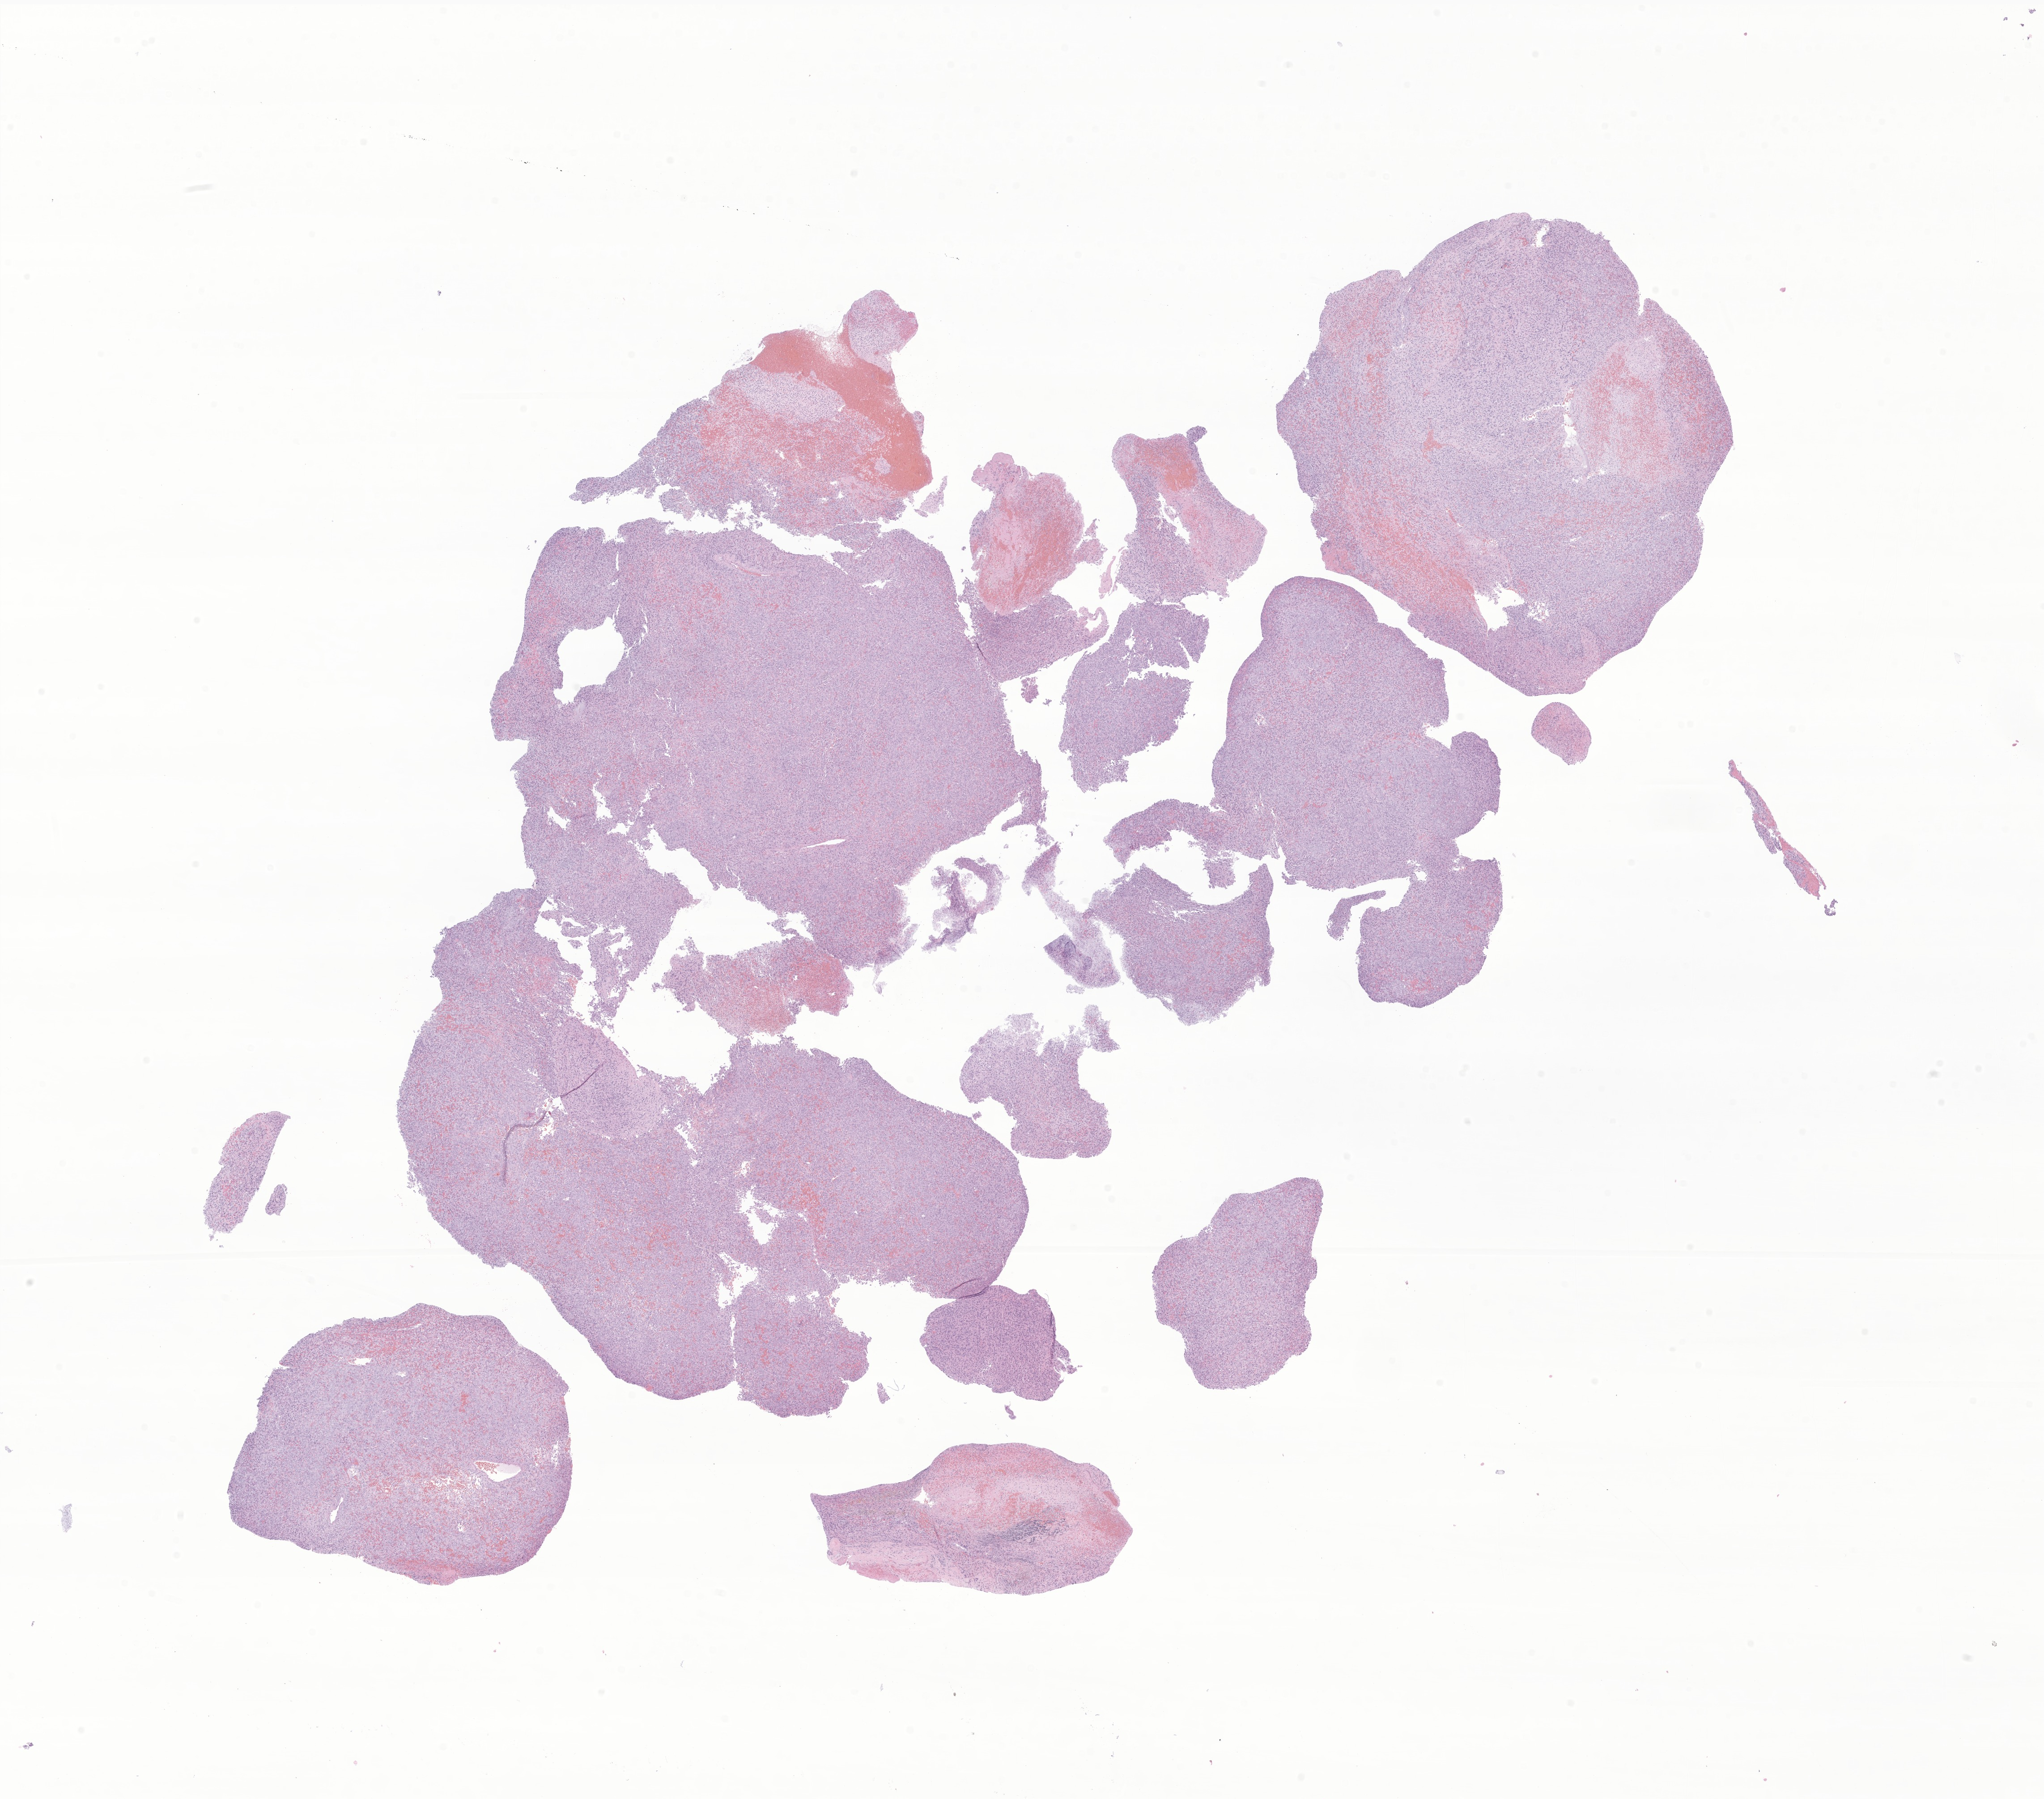
Whole-slide image, hematoxylin and eosin (H&E) stain of tumor tissue from the spinal cord, low-resolution overview of the scanned area, about 19.3 x 17.0 mm; formalin-fixed, paraffin-embedded (FFPE) tissue. Patient: female, age 87 months (7 years 3 months).
Diagnosis (ICD-O-3 morphology term): Atypical teratoid/rhabdoid tumor.